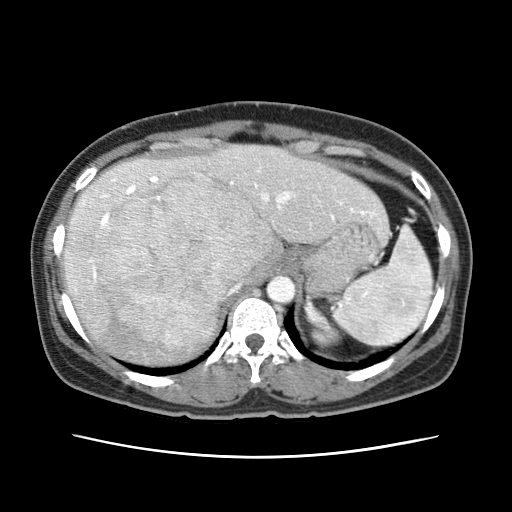
Contrast-enhanced abdominal CT (liver protocol), one axial slice; position 48 of 79 along the scan axis; reconstruction kernel STANDARD; 120 kVp; soft-tissue window (W 400 / L 40 HU); 2.5 mm slice thickness; 512 × 512 image matrix, field of view 340 × 340 mm. Case-level facts recorded for this patient, not image findings: diagnosis: hepatocellular carcinoma (patient treated with transarterial chemoembolisation; whether this scan precedes or follows treatment is not stated here); TNM stage (as recorded): Stage-I; Child-Pugh class: A; tumour nodularity: uninodular.
Structures marked on this image (semi-automatically segmented with operator editing):
- abdominal aorta: bounding box <266,276,295,302> (left, top, right, bottom; pixels)
- liver parenchyma outside the tumour (the mass and vessels are separate outlines, so this box may not span the whole liver): <62,144,386,364>
- mass: <99,178,271,346>
- liver vessels: <82,176,375,279>